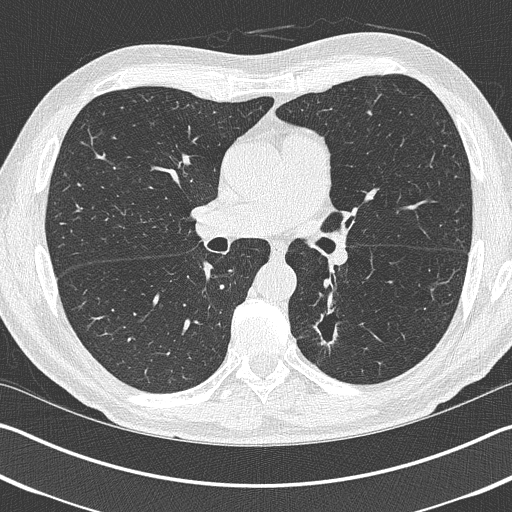
Low-dose screening chest CT, one axial slice. Slice 234 of 402 in the series (ordered by position). Reconstruction kernel B50f. 120 kVp. Lung window (W 1500 / L -600 HU). 1 mm slice thickness. 512 × 512 image matrix, field of view 340 × 340 mm.
Outlined on this slice (expert manual segmentation):
- lesion 1 (tumor, lower lobe of left lung): bounding box (x1, y1, x2, y2) in pixels: (313, 308, 338, 347)